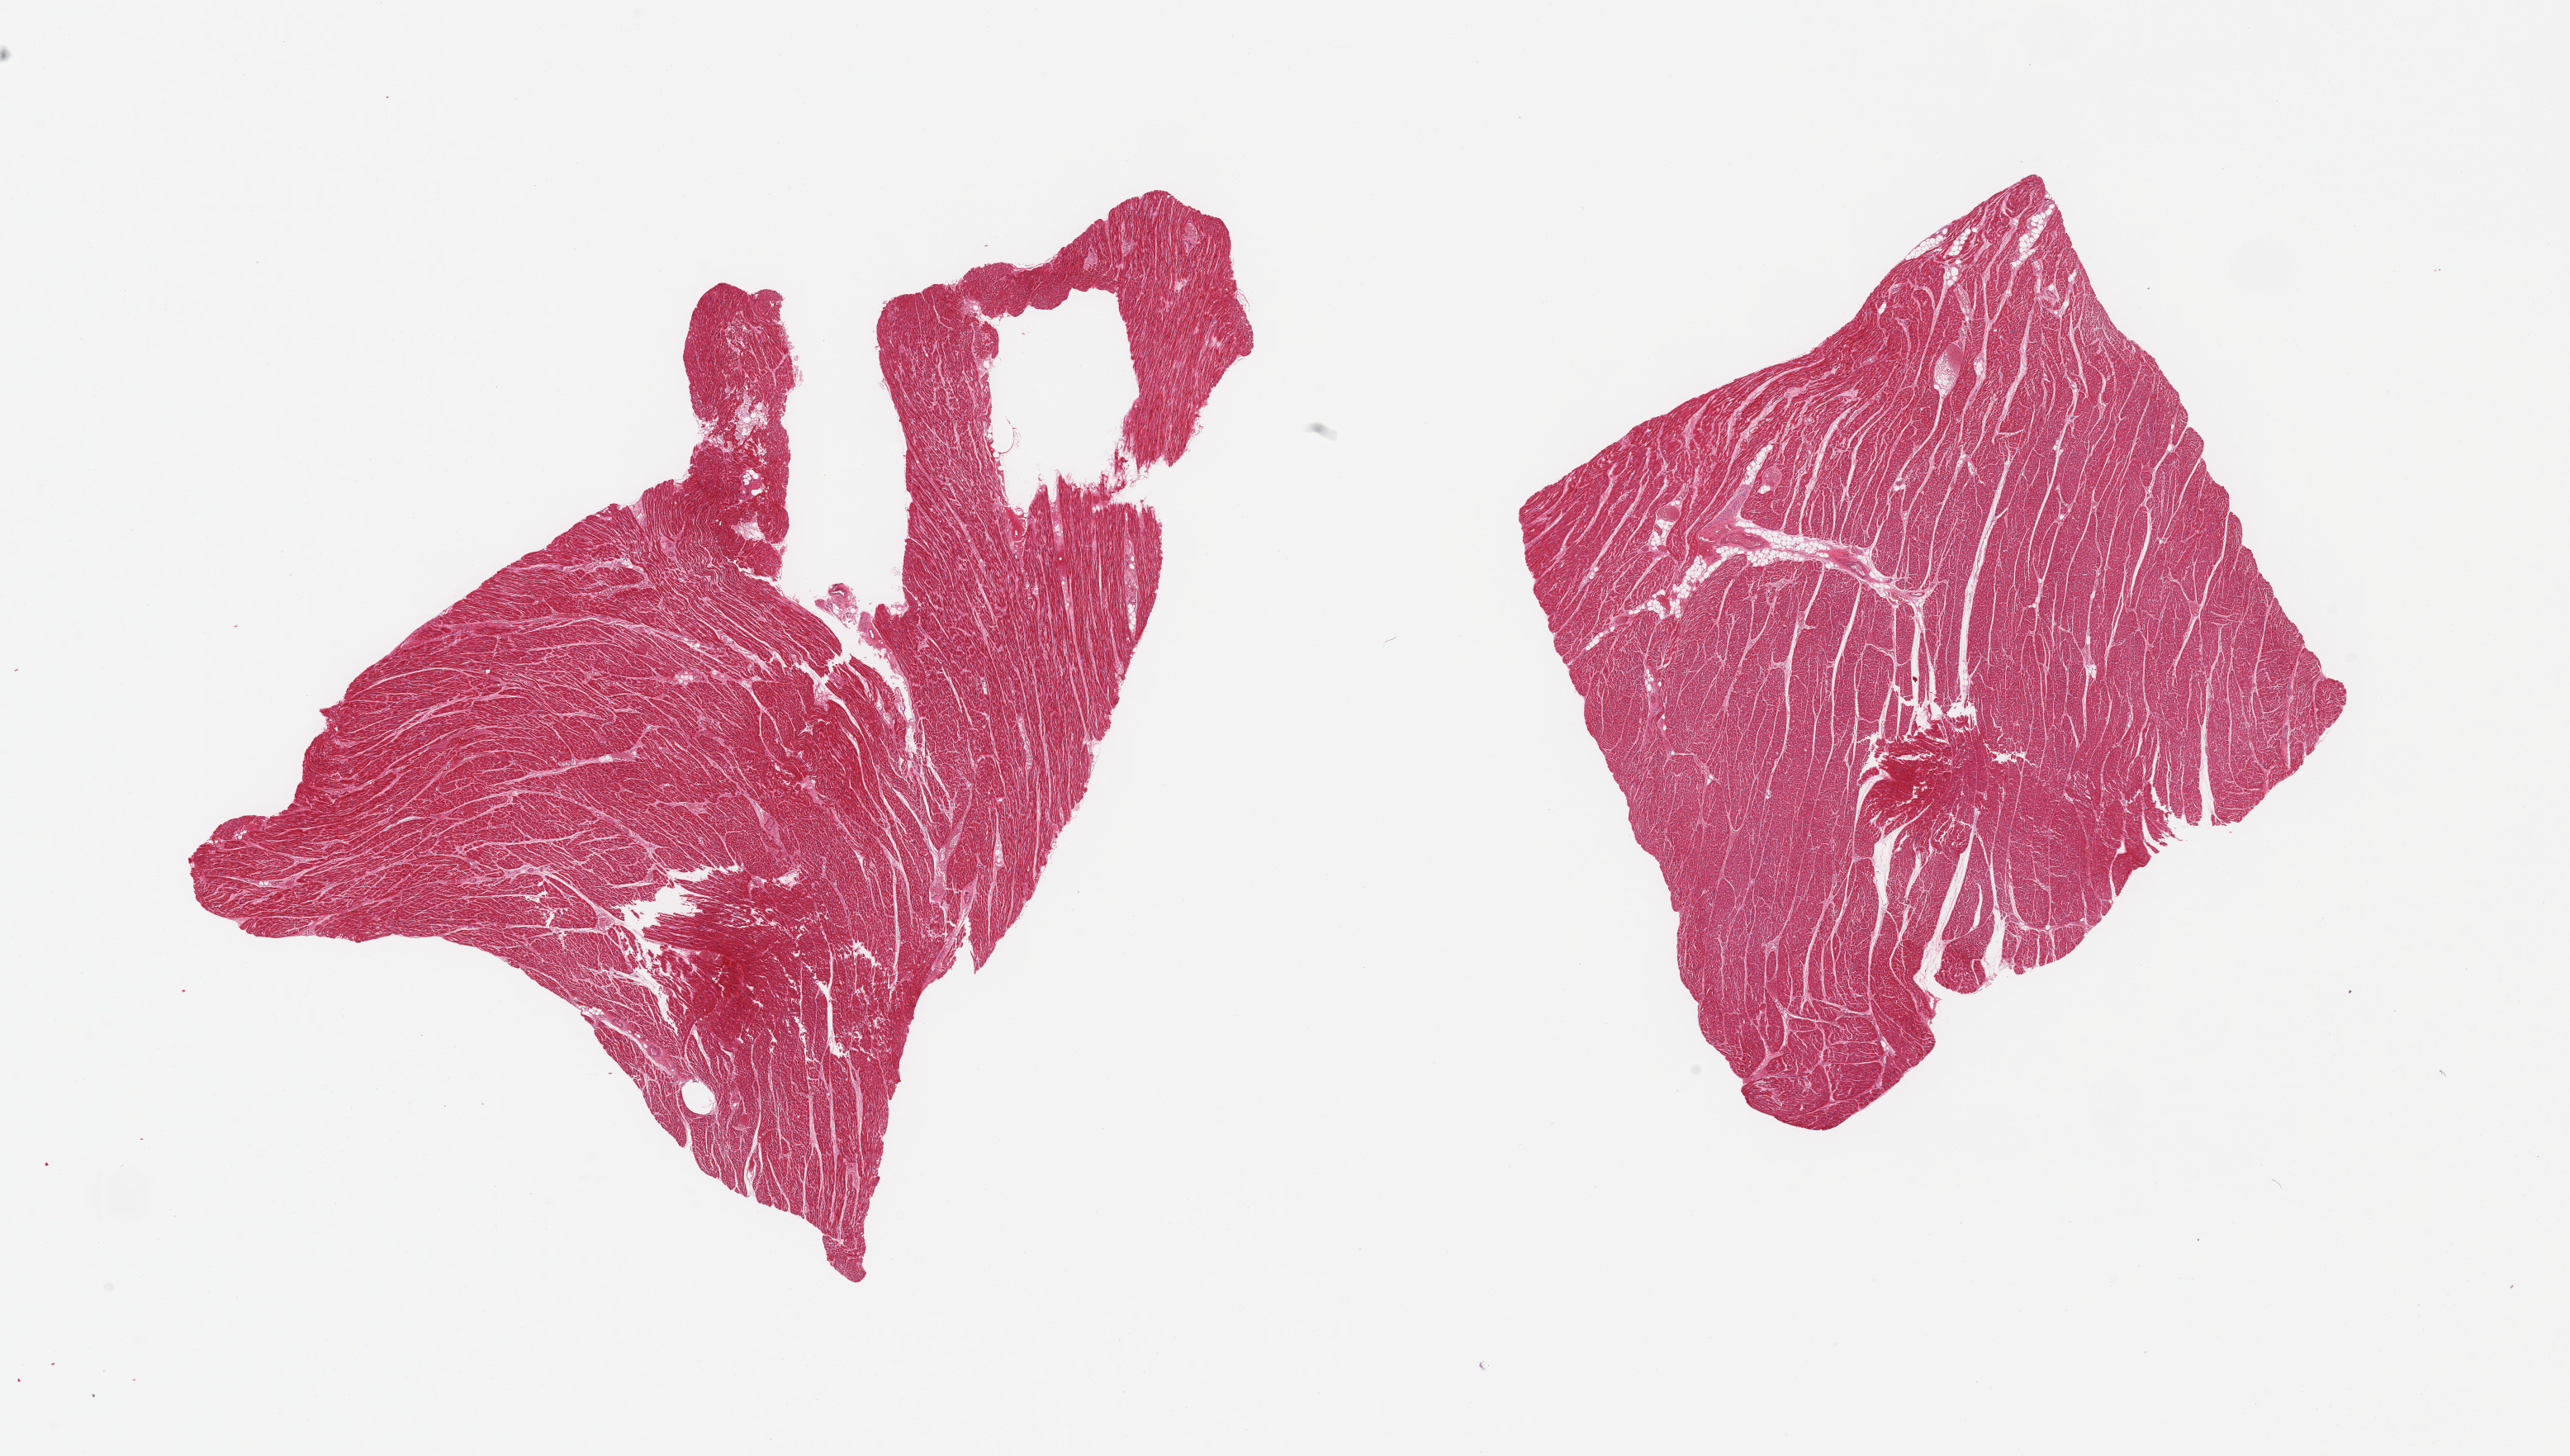
Hematoxylin and eosin (H&E) whole-slide image — whole scanned area (about 24.6 x 13.9 mm, slide scanned at 20x) shown as a low-resolution overview, PAXgene-fixed paraffin-embedded (PFPE) section, sampled site (target tissue): heart, donor tissue sample.
Review note (as recorded): 2 pieces, mild interstitial fibrosis/chronic ischemic changes.